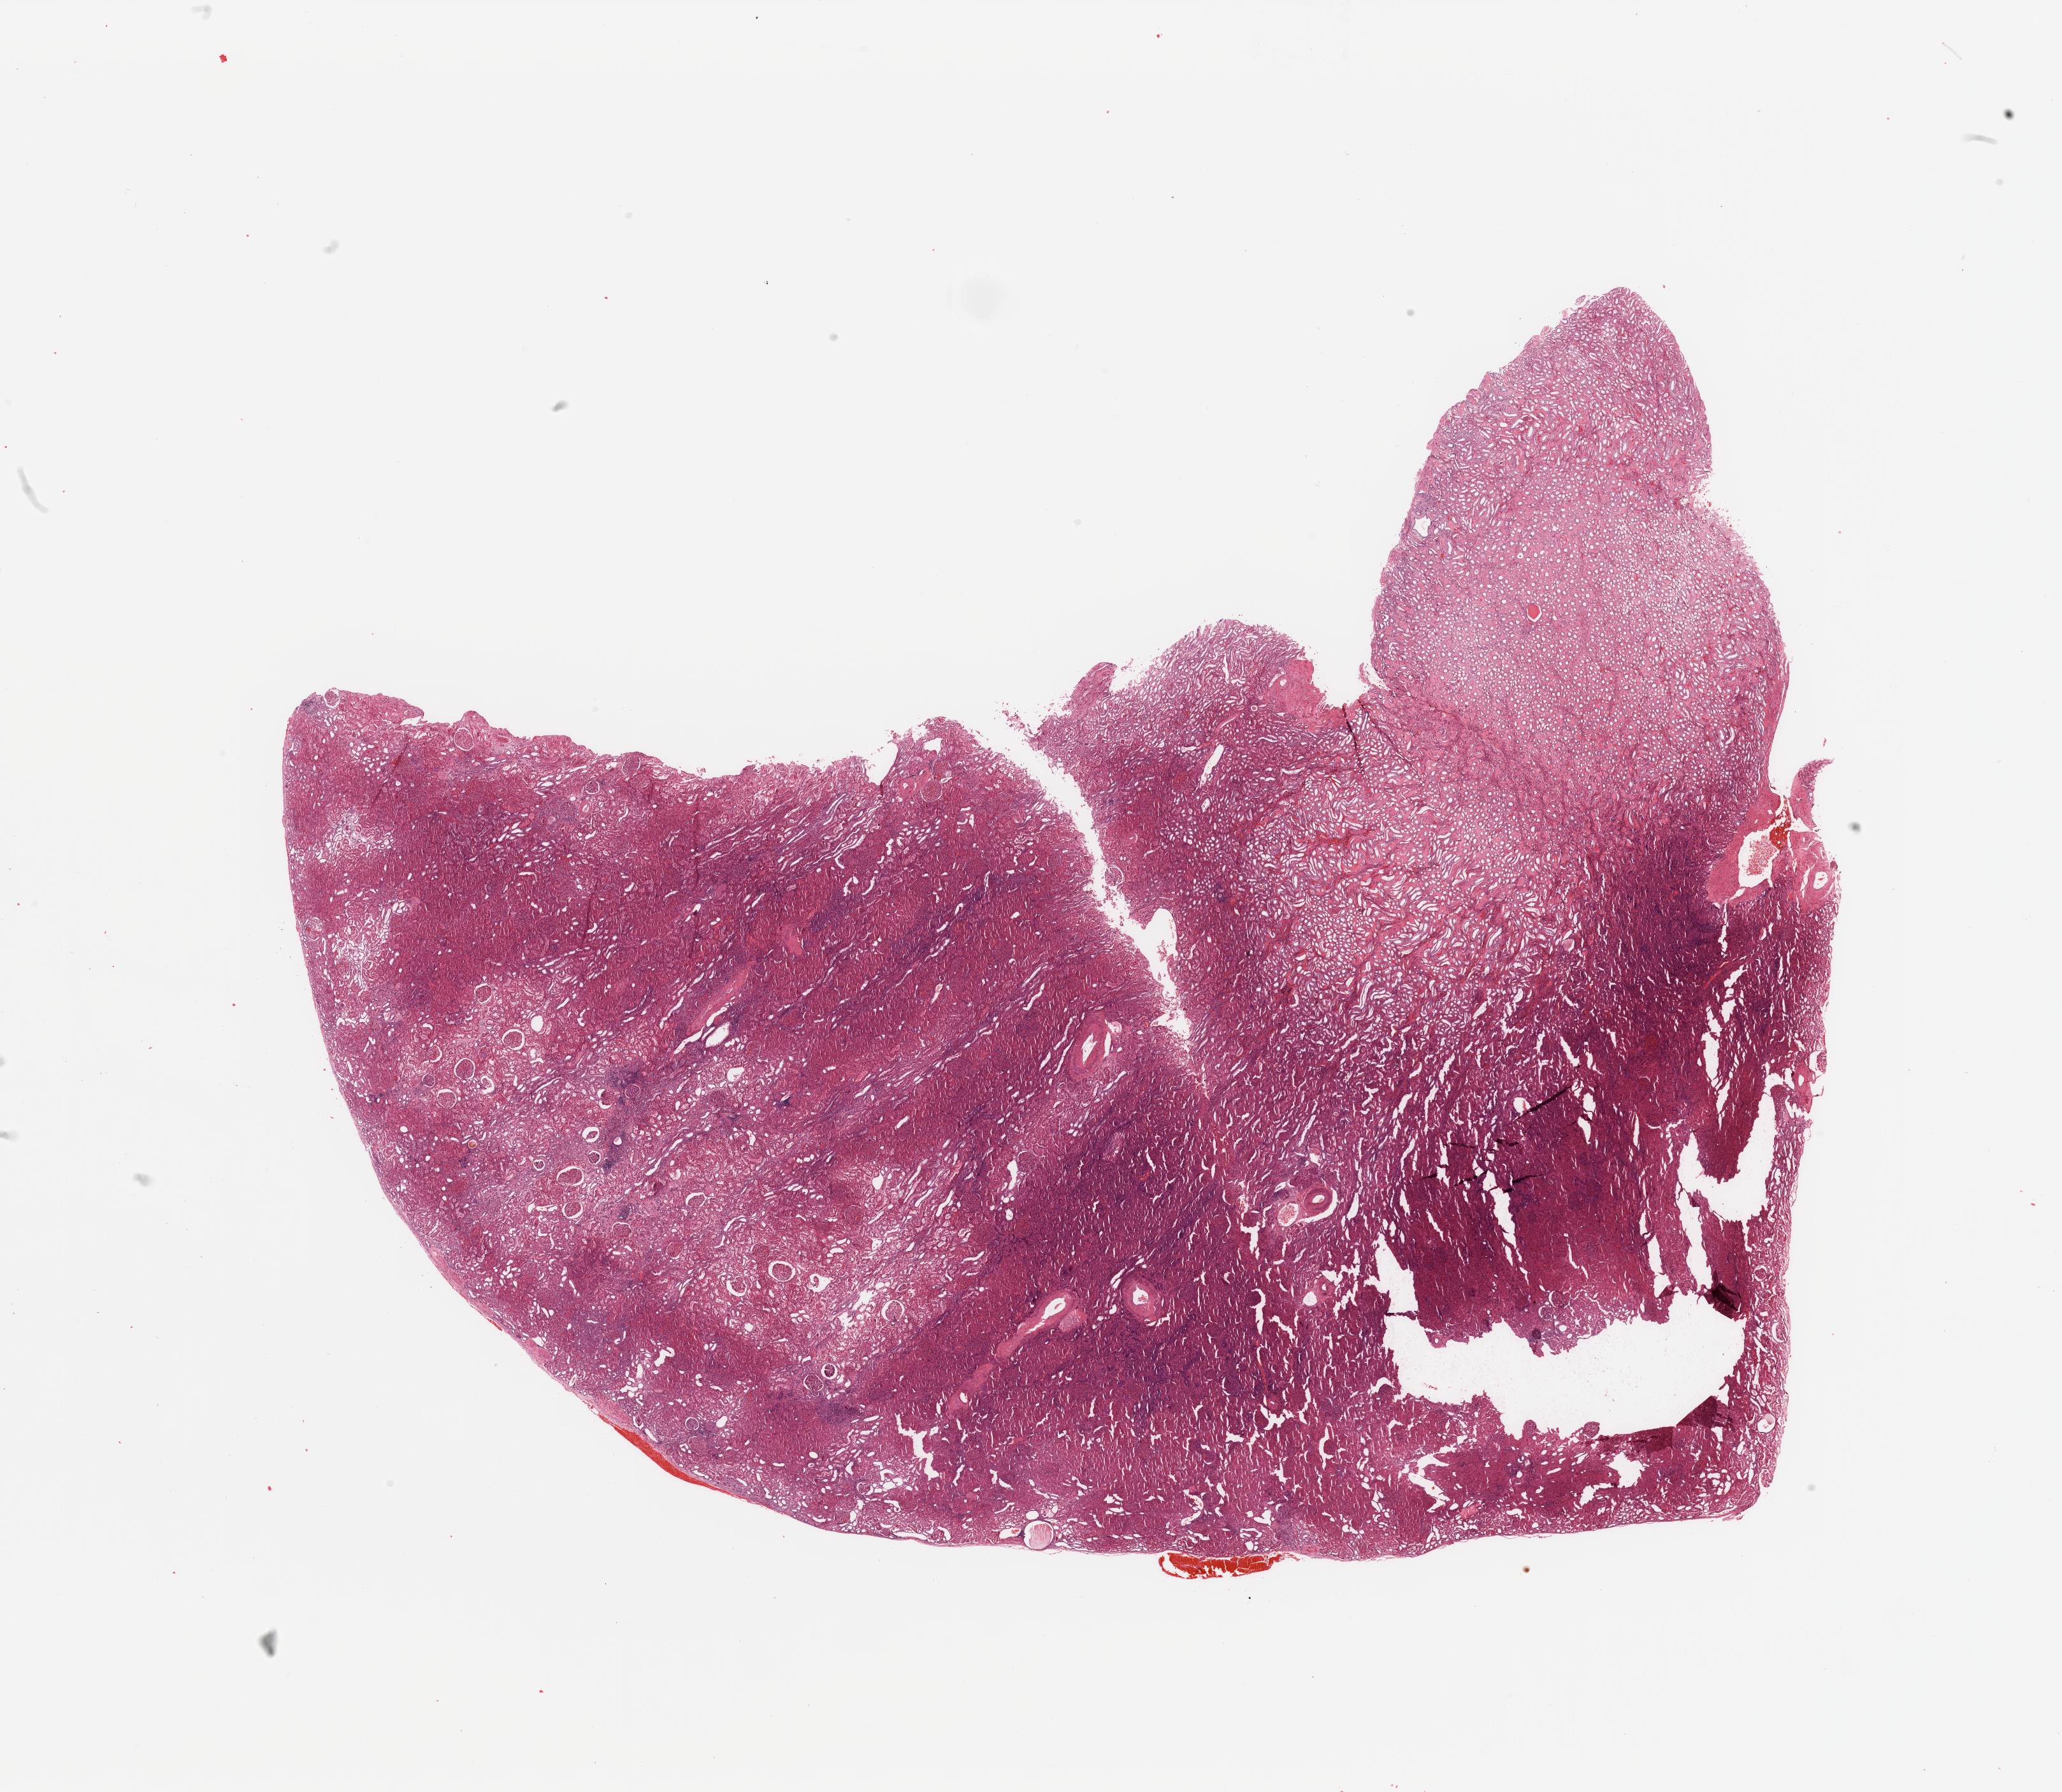
H&E whole-slide image, whole scanned area (about 25.6 x 22.2 mm) shown as a low-resolution overview; normal (non-tumour) tissue sample, sampled site: kidney. 53-year-old male patient.
This section: normal (non-tumour) tissue from the same patient. Patient diagnosis: Renal cell carcinoma, NOS.